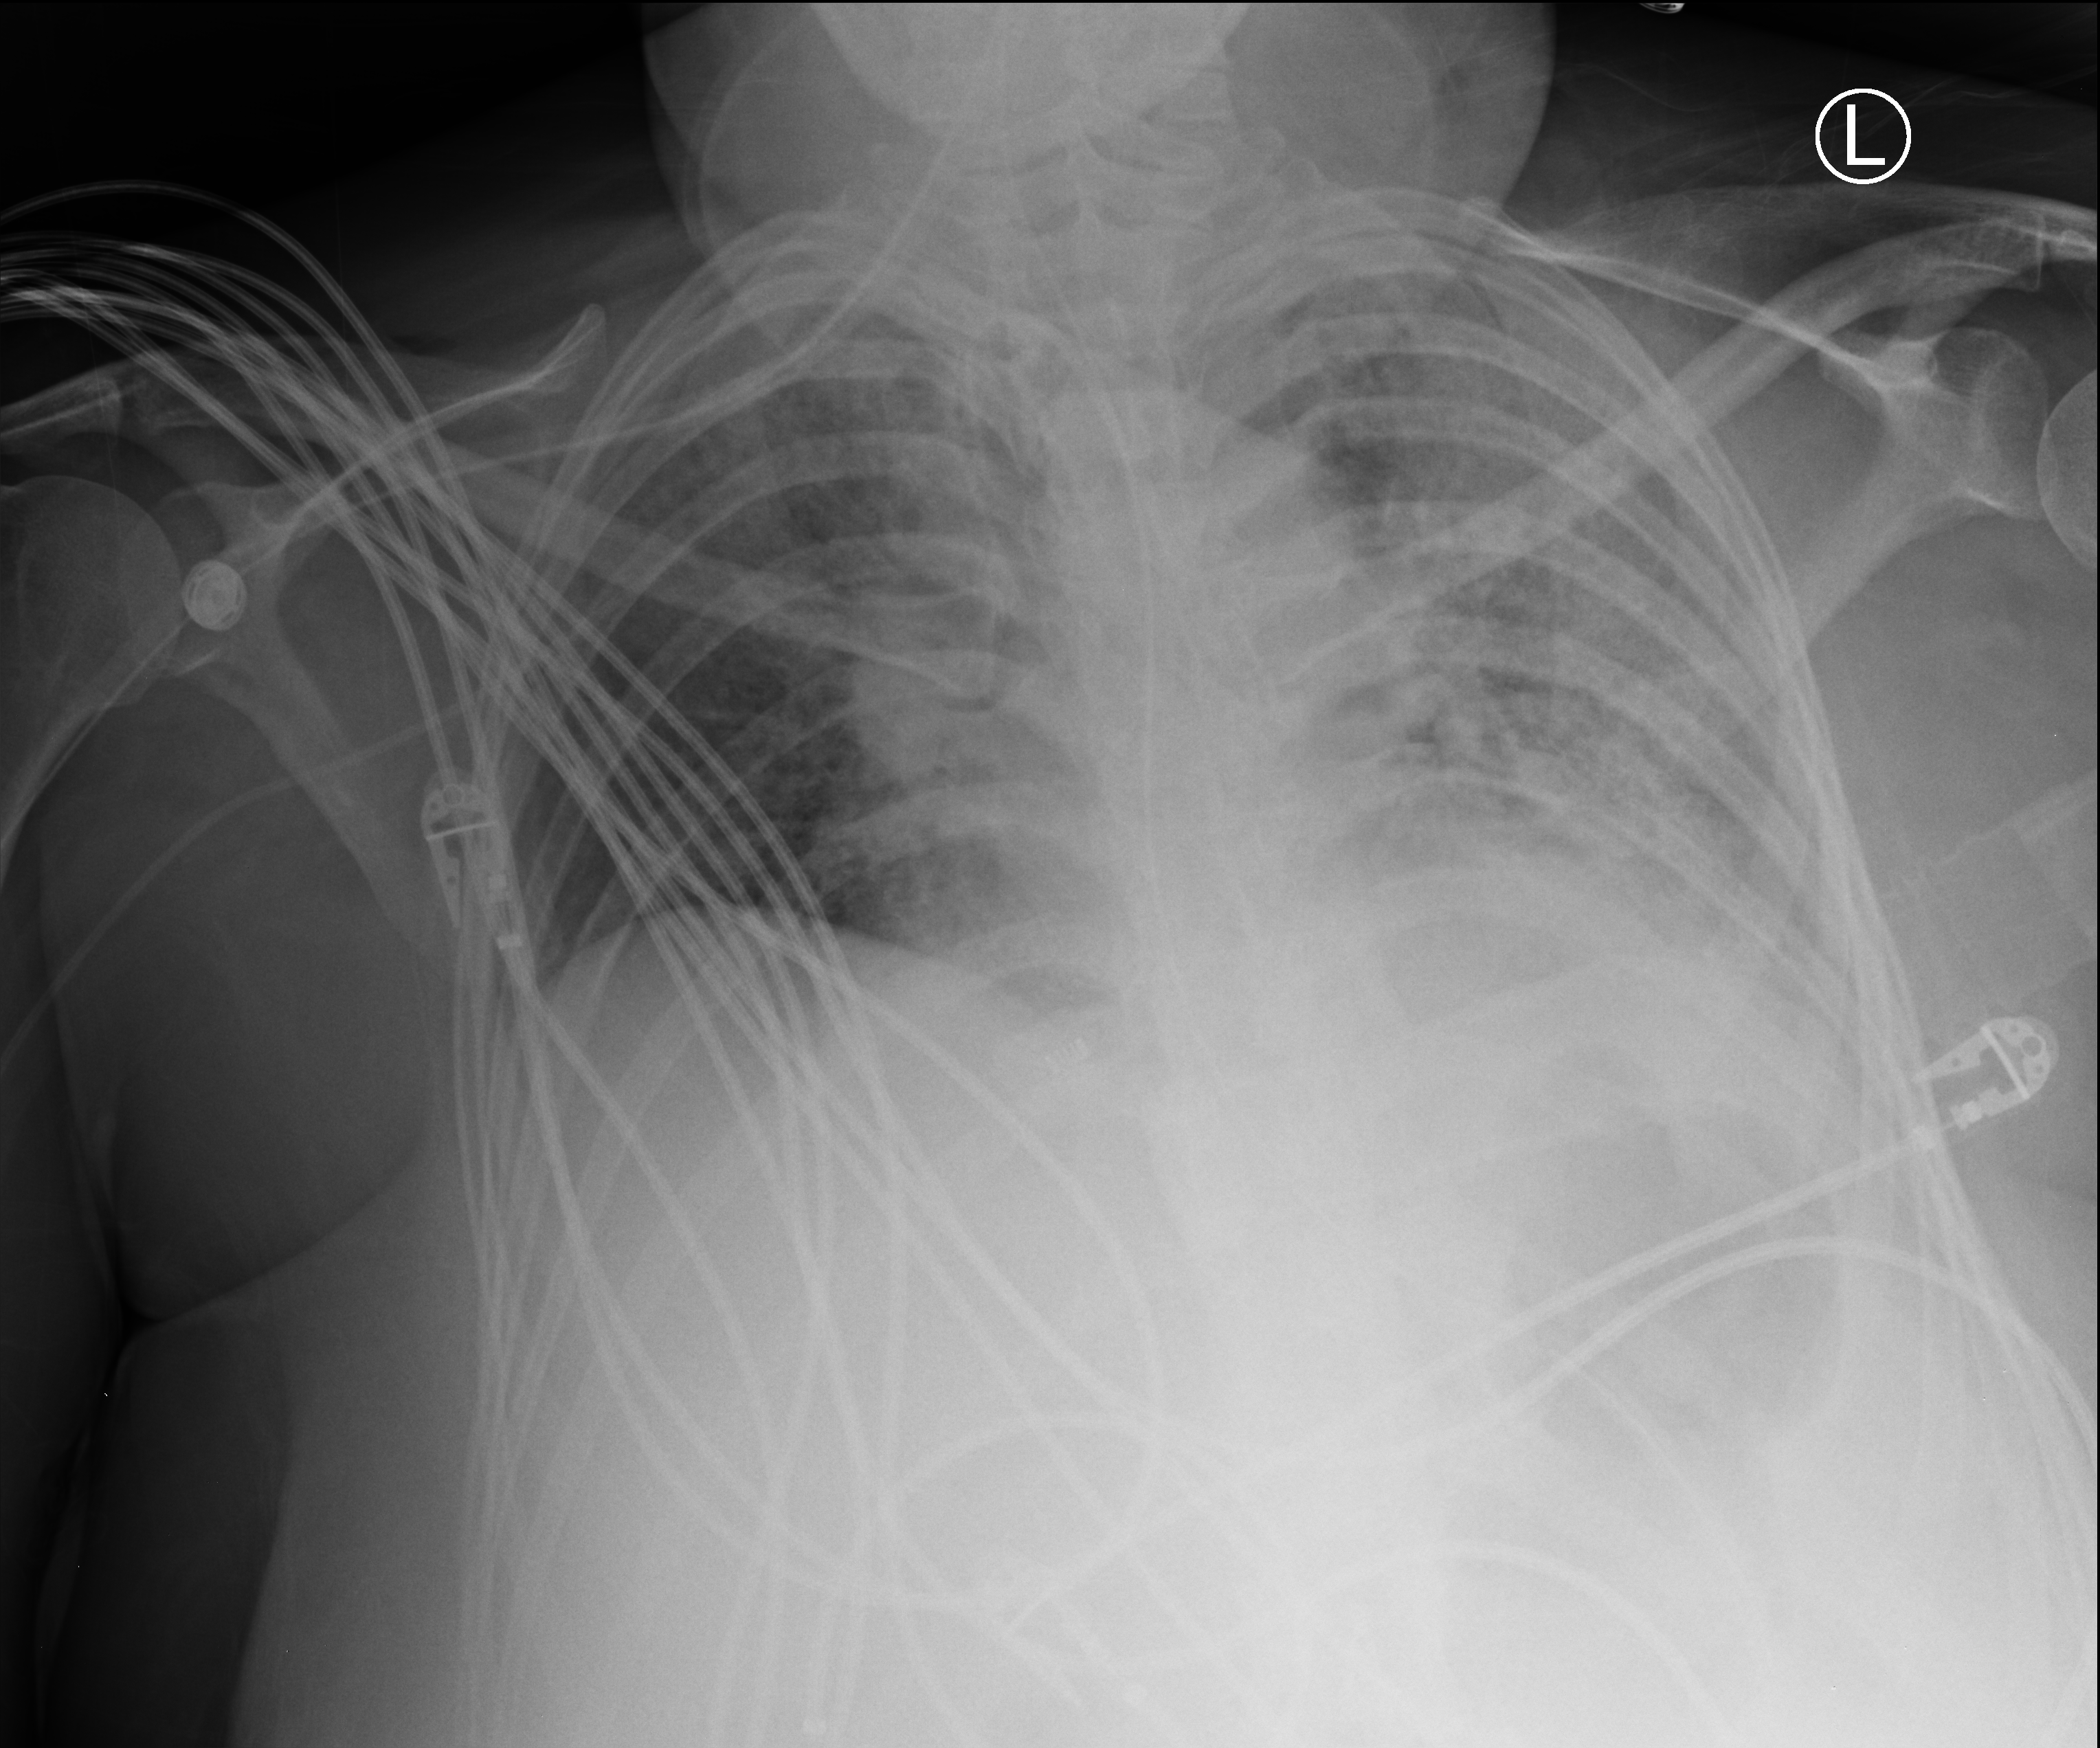
Bedside chest radiograph (computed radiography), anteroposterior (AP) projection. Patient hospitalised with COVID-19; female, aged 18–59 years.
Admission-level facts for this patient (not findings on this image; timing relative to this image not recorded):
- other chronic lung disease (admission record): yes
- hypertension (admission record): no
- COPD (admission record): no